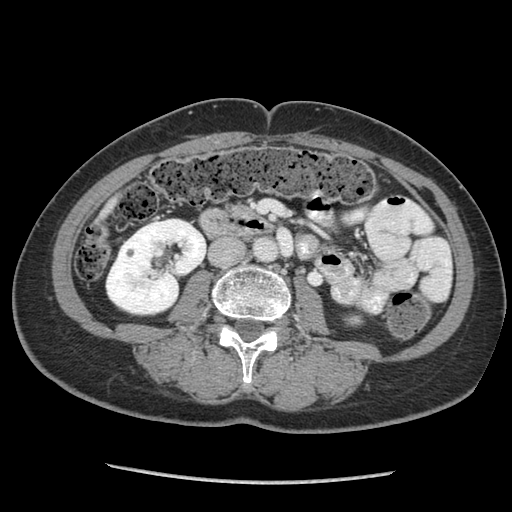
Contrast-enhanced abdominal CT (liver protocol), one axial slice. Slice 13 of 105 in the series (ordered by position). Reconstruction kernel STANDARD. 140 kVp. Soft-tissue window (W 400 / L 40 HU). 2.5 mm slice thickness. 512 × 512 image matrix. From the clinical record (not read from this slice): diagnosis: hepatocellular carcinoma (patient treated with transarterial chemoembolisation; whether this scan precedes or follows treatment is not stated here); TNM stage (as recorded): Stage-I; Child-Pugh class: A; tumour differentiation: moderately differentiated; tumour nodularity: uninodular.
Structures marked on this image (semi-automatic segmentation, software-assisted and operator-edited):
- liver parenchyma outside the tumour (the mass and vessels are separate outlines, so this box may not span the whole liver): bounding box (x1, y1, x2, y2) in pixels: (98, 200, 114, 220)